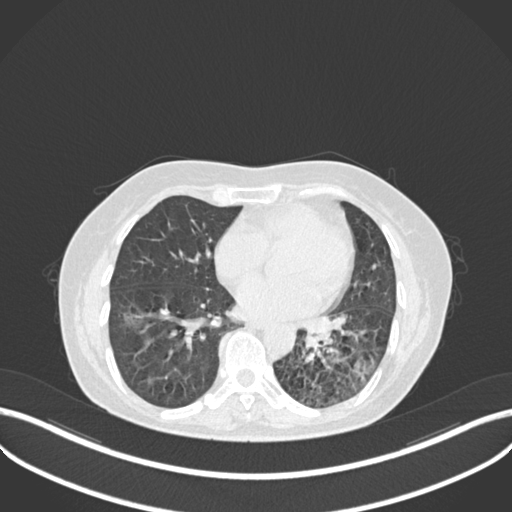
Chest CT, one axial slice. Position 107 of 270 along the scan axis. Reconstruction kernel B30f. 120 kVp. Lung window (W 1500 / L -600 HU). 512 × 512 image matrix, field of view 400 × 400 mm. Female patient, age 63 years. From the clinical record (not read from this slice): clinical TNM (as recorded): T1b N0 M0; histopathological grade: G2-3.
Annotated regions visible in this slice (bounding box drawn by a radiologist):
- lung tumour (recorded histology: adenocarcinoma): bounding box <297,313,337,355> (left, top, right, bottom; pixels)